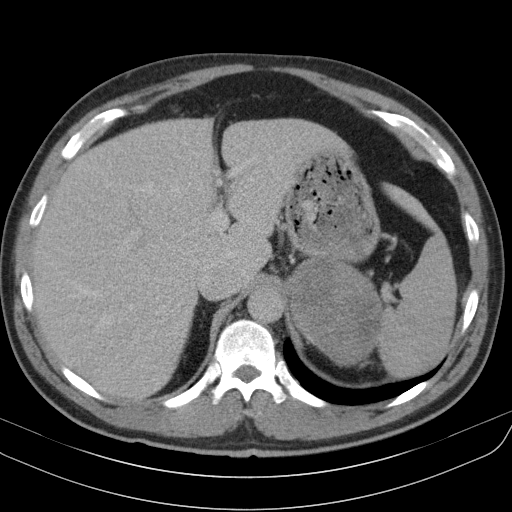
Contrast-enhanced abdominal CT, one axial slice; slice 77 of 91 in the series (ordered by position); 130 kVp; intravenous contrast given; soft-tissue window (W 400 / L 40 HU); 512 × 512 image matrix, field of view 370 × 370 mm. Patient: male, 51 years. Case-level facts recorded for this patient, not image findings: diagnosis: adrenocortical carcinoma; tumour side: left adrenal; tumour size at pathology: 18 cm; Ki-67 index: 40 %; stage (as recorded): 3.
Structures marked on this image (semi-automatic segmentation, software-assisted and operator-edited):
- mass: bounding box [x1, y1, x2, y2] px = [287, 260, 382, 365]